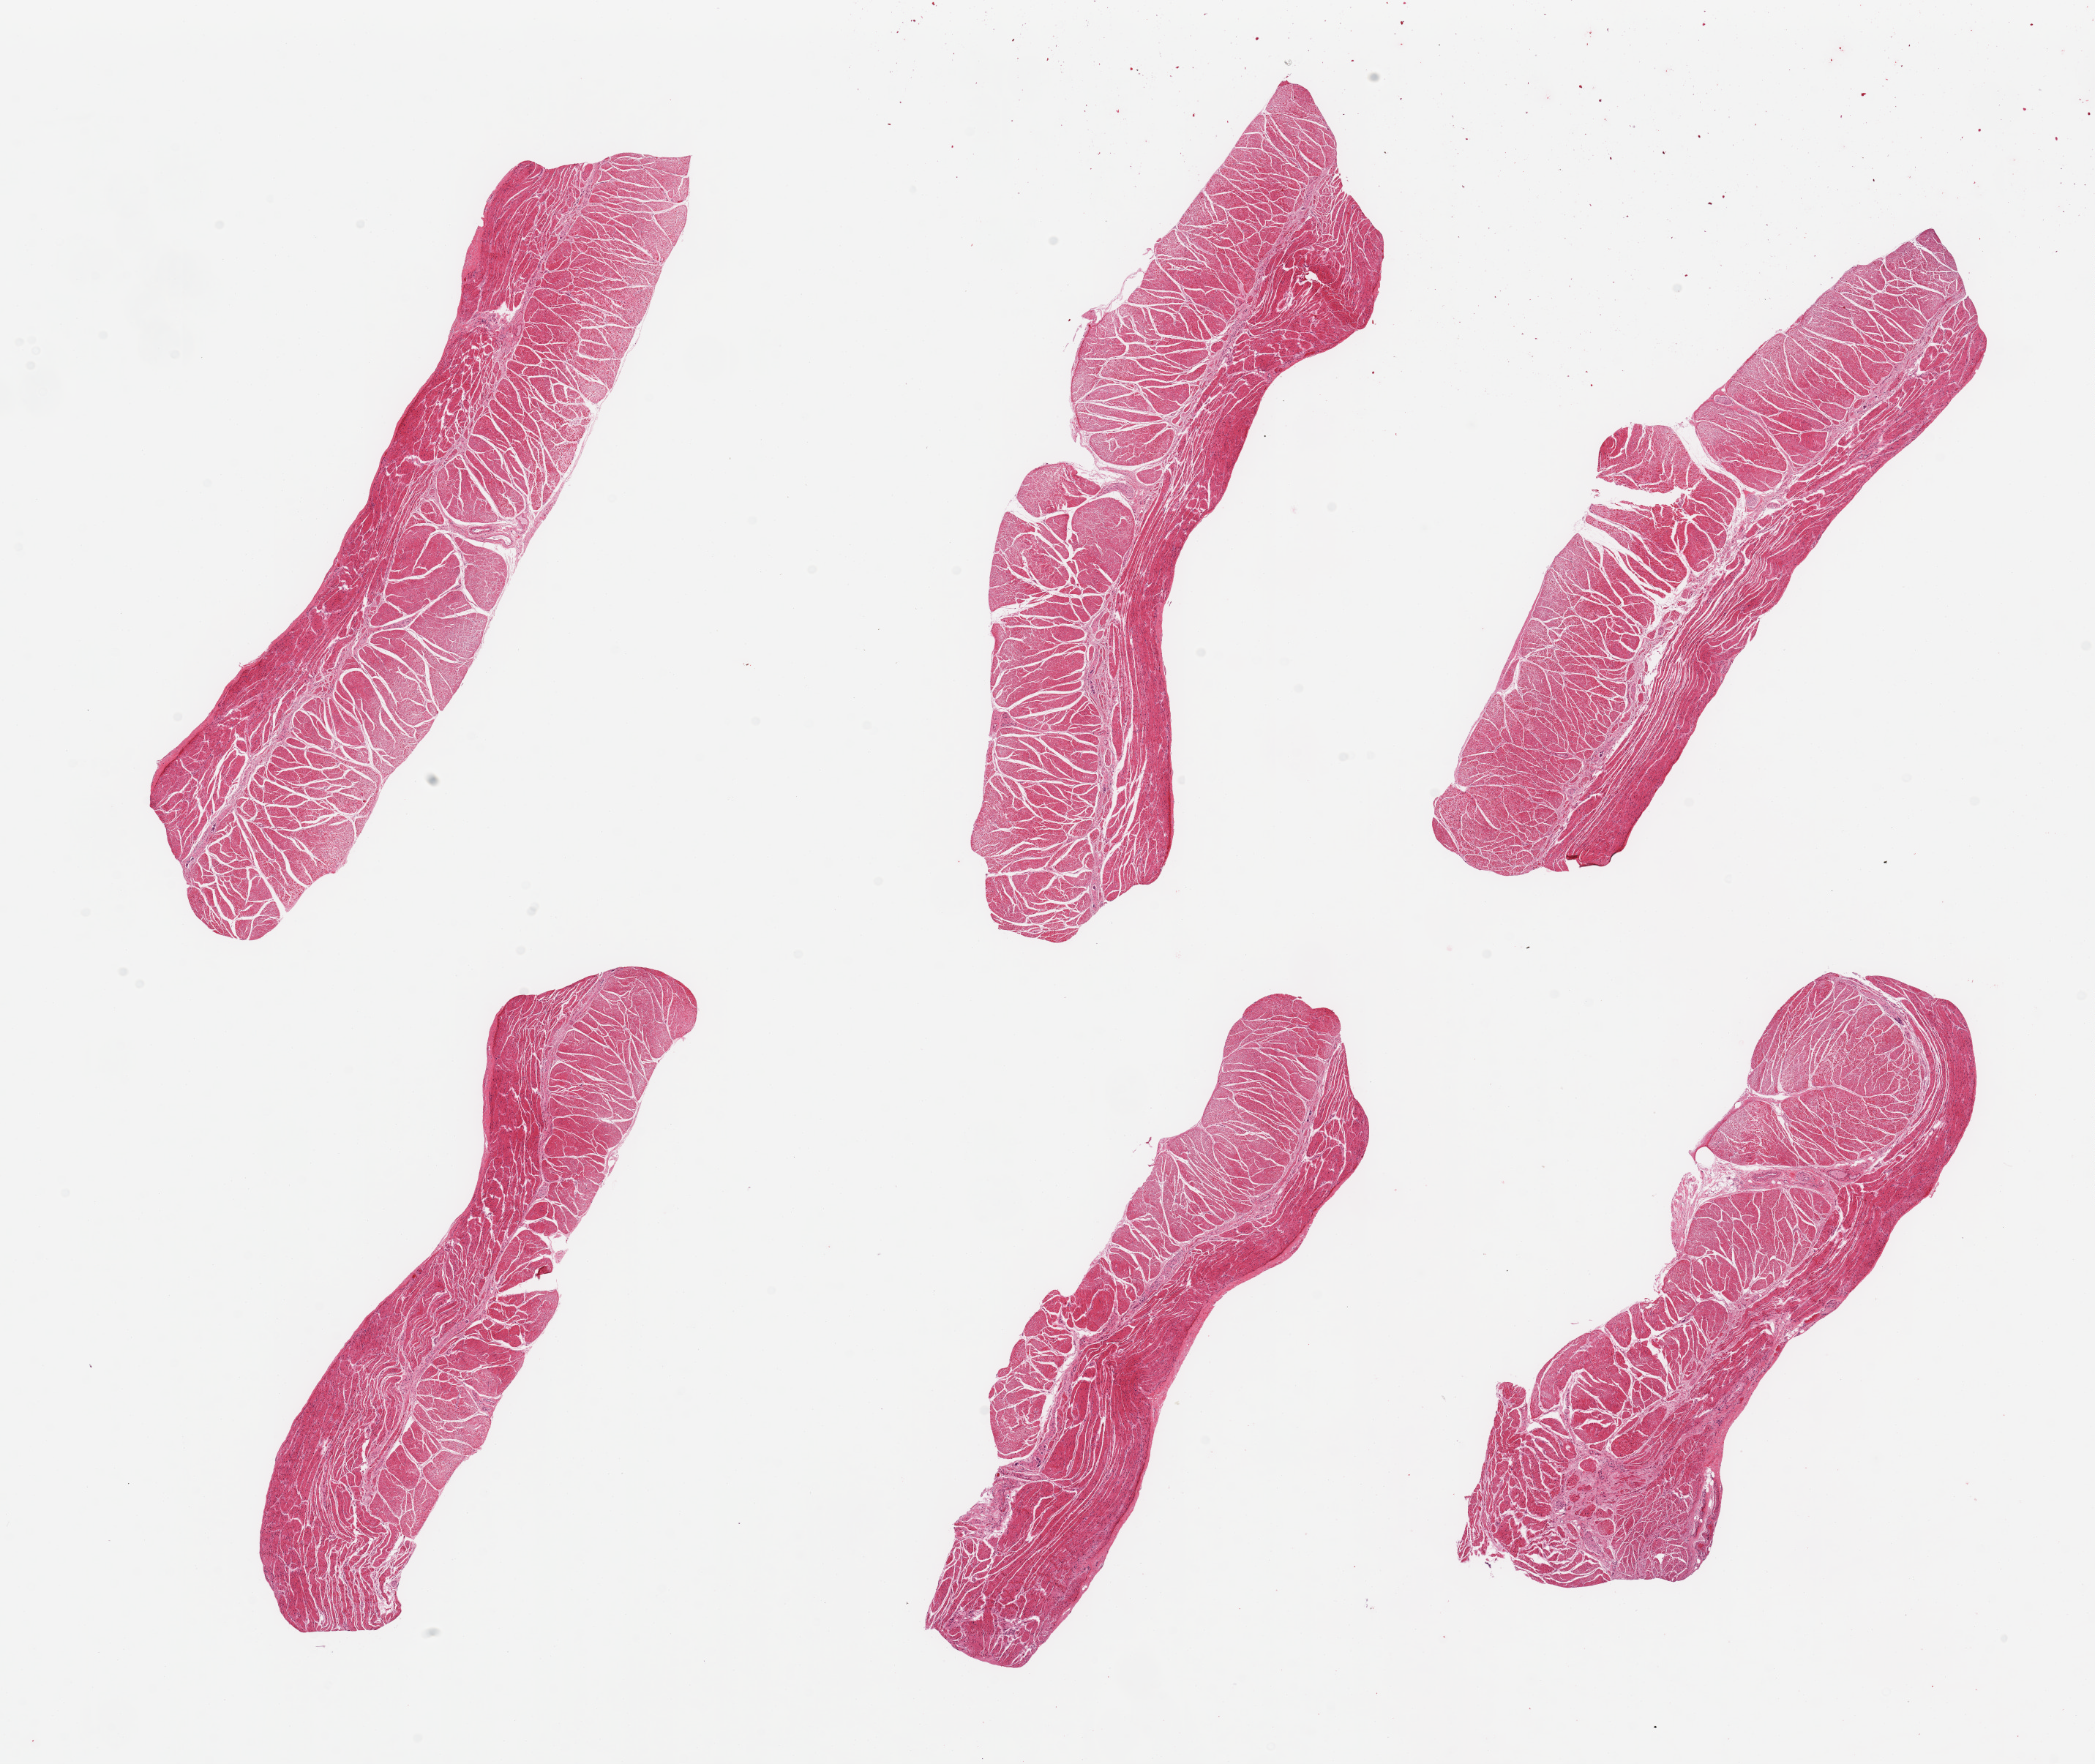
Whole-slide image, haematoxylin and eosin stain, brightfield, a low-resolution overview of the entire scanned area, about 22.6 x 19.1 mm (slide scanned at 20x). PAXgene-fixed, paraffin-embedded tissue. Sampled site (target tissue): esophageal muscle. Donor tissue sample. Male donor.
Pathologist's review note for this sample: 6 pieces; well dissected muscularis.